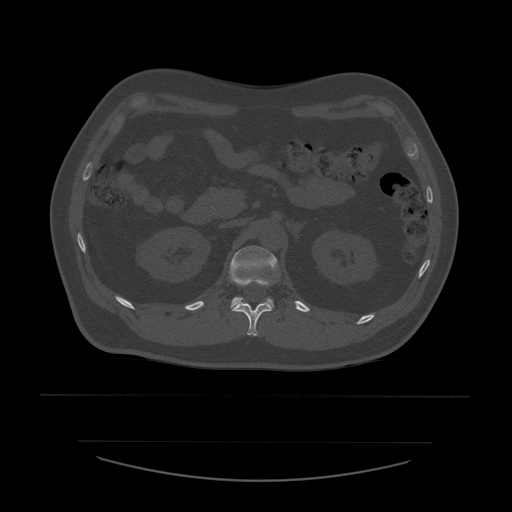
CT including the spine, one axial slice. Slice 240 of 532 in the series (ordered by position). Bone window (W 1800 / L 400 HU). 1.25 mm slice thickness. 512 × 512 image matrix, field of view 441 × 441 mm. Patient age 44 years. Case-level facts recorded for this patient, not image findings: primary cancer: soft tissue sarcoma.
Outlined on this slice (semi-automatically segmented with operator editing):
- L1 vertebra: bounding box (x1, y1, x2, y2) in pixels: (230, 246, 278, 312)
- T12 vertebra: (233, 284, 273, 336)